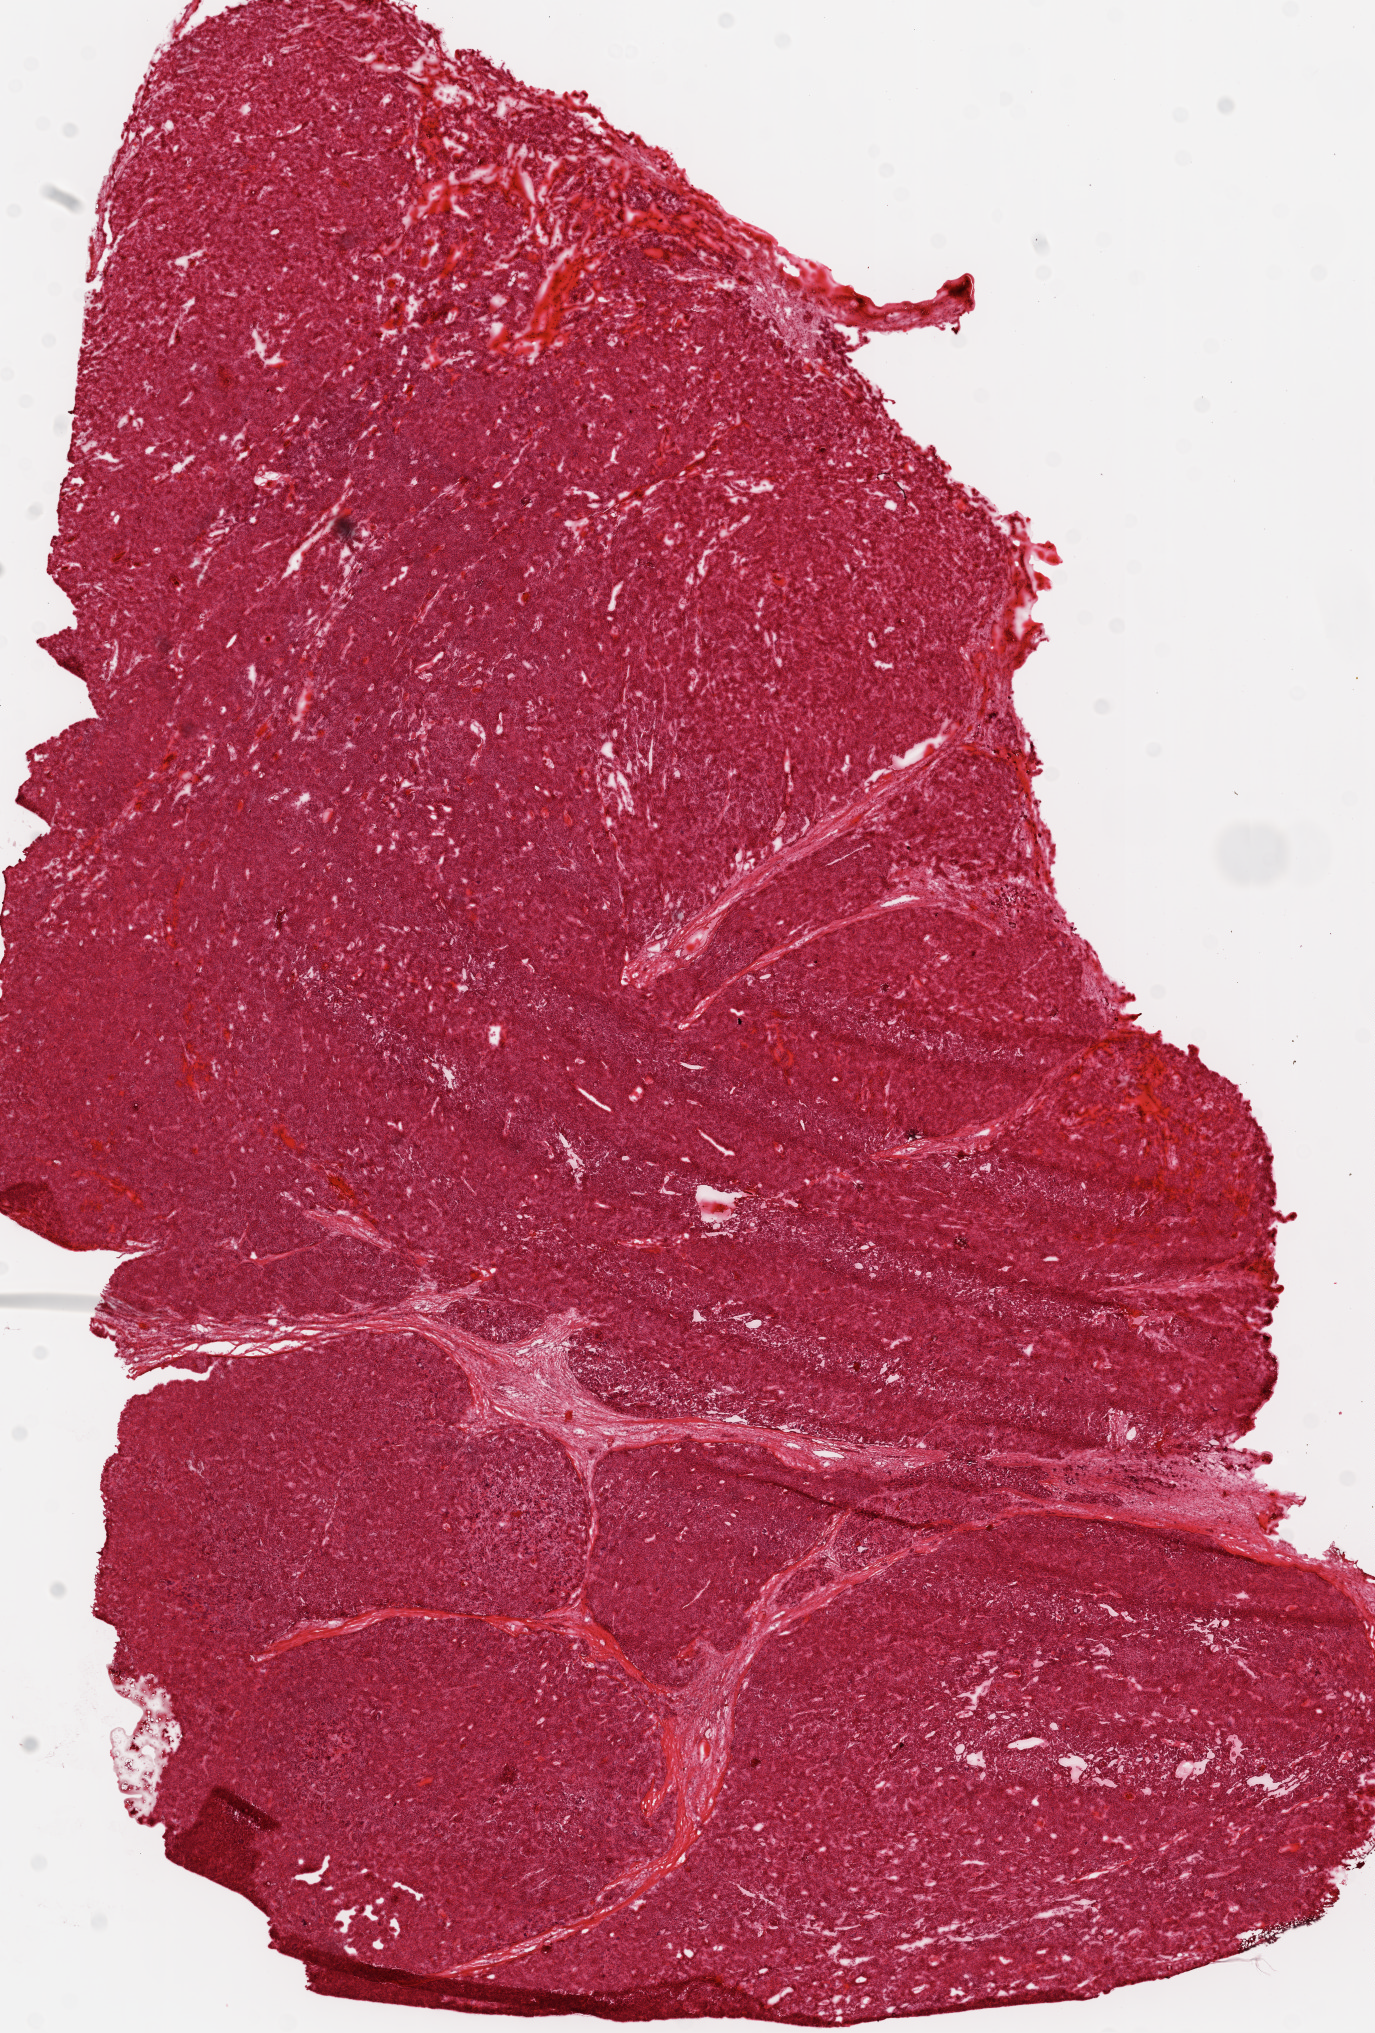
Whole-slide histology image, H&E — whole scanned area (about 11.0 x 16.3 mm, acquisition: 20x scan) shown as a low-resolution overview, frozen section from the top of the tissue portion, sample: primary tumour, ovary. Female patient; age at initial diagnosis 60 years. Composition of this section per pathologist review: tumour cells 98%, tumour nuclei 99%.
Pathologic diagnosis: Serous cystadenocarcinoma, NOS.